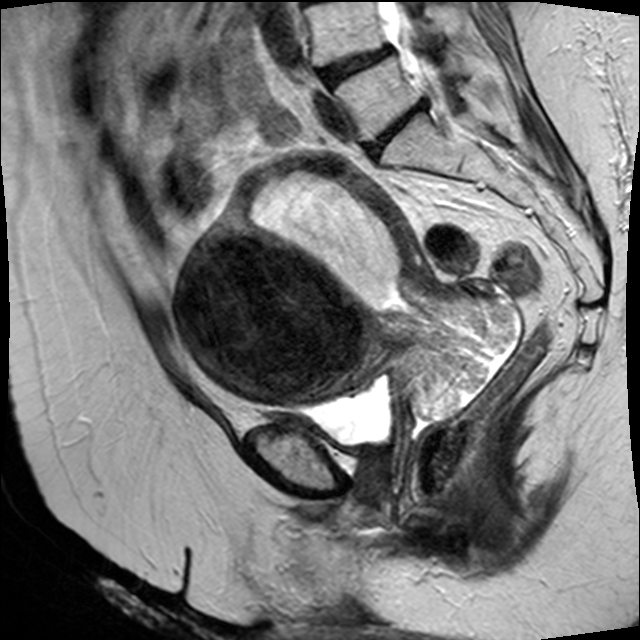
Pelvic MRI for cervical cancer, one sagittal slice; T2-weighted; 1.5 T; TE 89 ms, TR 4610 ms; 4 mm slice thickness; 640 × 640 image matrix, field of view 260 × 260 mm. Patient: female, 50 years.
Structures marked on this image (expert manual segmentation):
- uterus and cervix: bounding box [x1, y1, x2, y2] px = [173, 150, 518, 420]